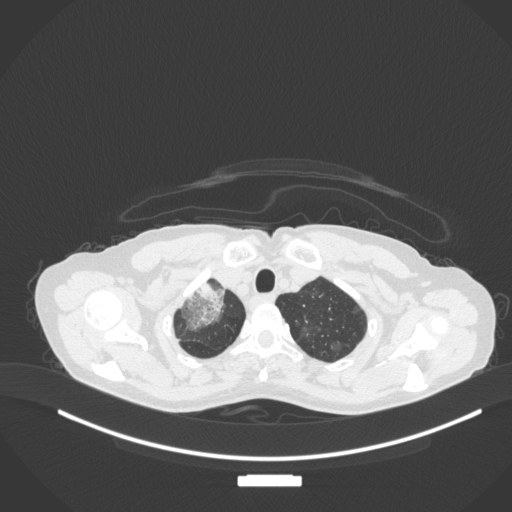
Chest CT, one axial slice. Position 292 of 311 along the scan axis. Reconstruction kernel B31f. 120 kVp. Lung window (W 1500 / L -600 HU). 1 mm slice thickness. 512 × 512 image matrix. Female patient, age 59 years. From the clinical record (not read from this slice): clinical TNM (as recorded): T3 N0 M0.
Structures marked on this image (bounding box drawn by a radiologist):
- lung tumour (recorded histology: adenocarcinoma): bounding box <173,273,230,331> (left, top, right, bottom; pixels)